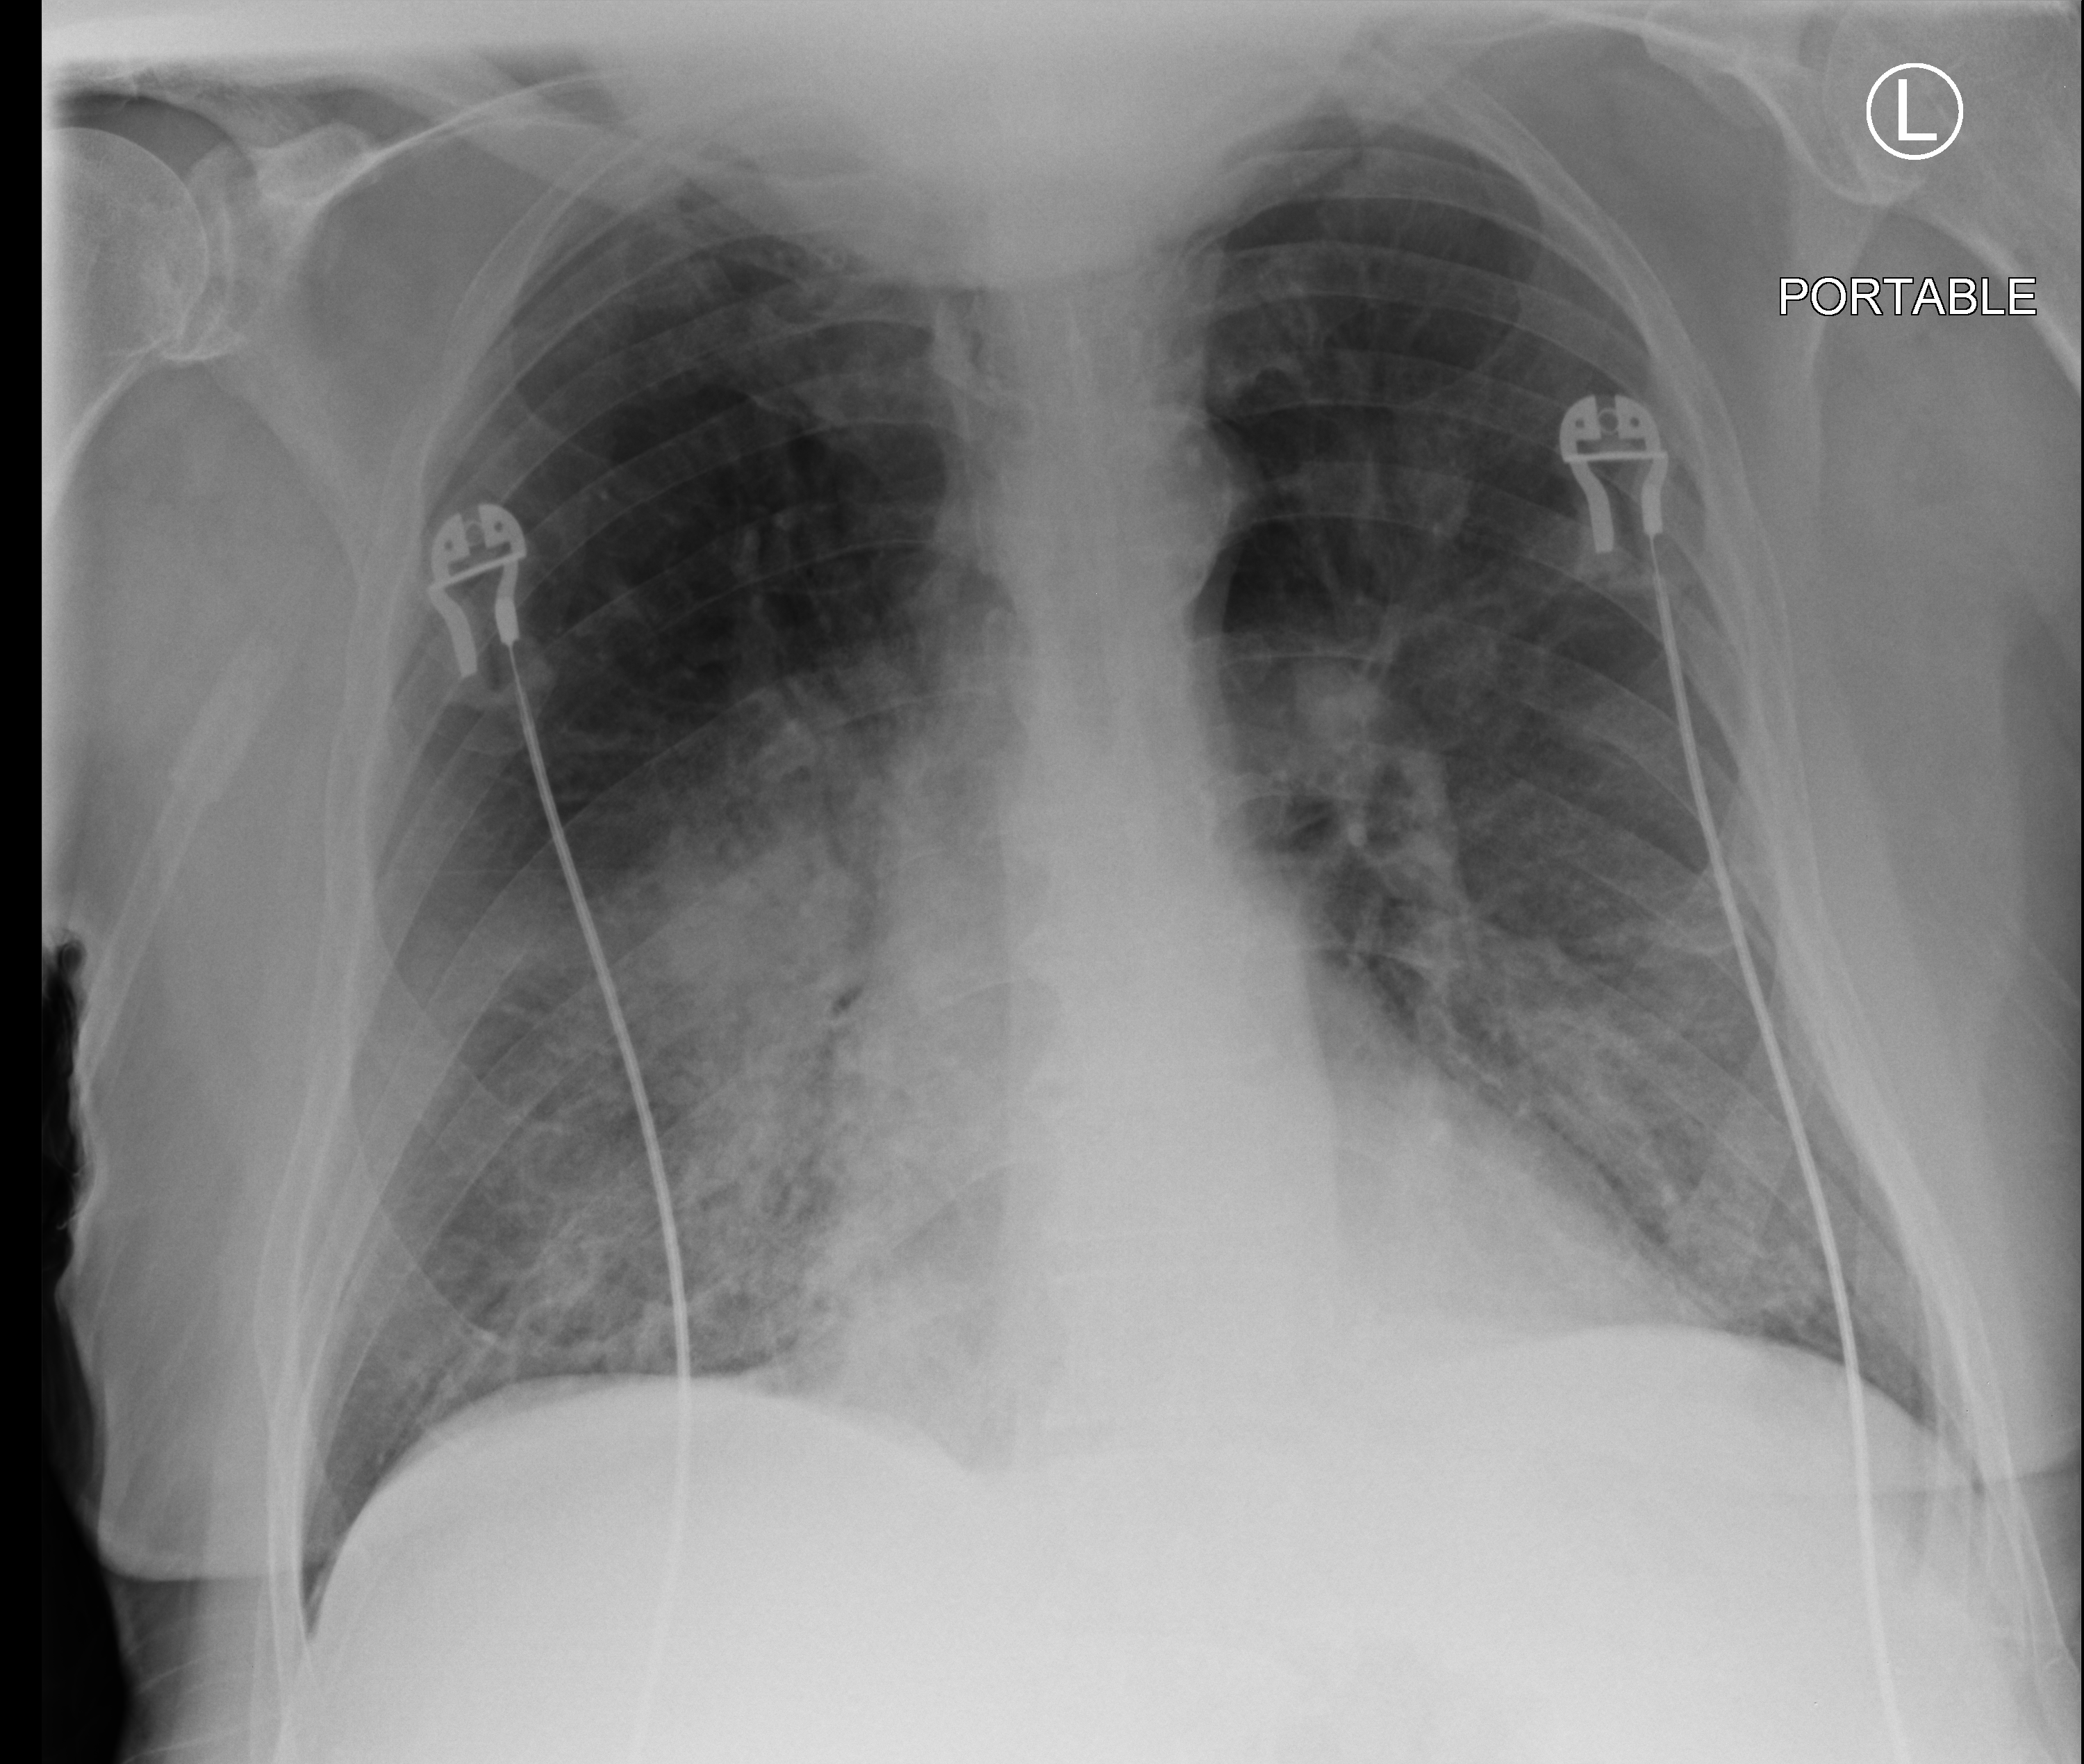
Portable chest radiograph; anteroposterior (AP) projection. Male patient hospitalised with COVID-19, age 60–74 years.
Hospital-stay facts (about this admission, not read from this image; timing relative to this image not recorded): diabetes (admission record): no.